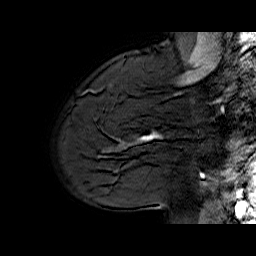
Breast MRI (dynamic contrast-enhanced), one sagittal slice. Slice 50 of 70 in the series (ordered by position). Dynamic contrast-enhanced series, time point 2 of 6 at this slice position (early post-contrast). 1.5 T. TE 6.5 ms, TR 33 ms. 4 mm slice thickness. 256 × 256 image matrix, field of view 200 × 200 mm. Female patient. From the clinical record (not read from this slice): setting: breast cancer imaged before/during neoadjuvant chemotherapy; receptor status: HER2-positive.
Outlined on this slice (semi-automatic segmentation, software-assisted and operator-edited):
- analysis volume of interest (the breast-tissue region the enhancement analysis was run in; not a lesion): bounding box <113,112,174,170> (left, top, right, bottom; pixels)
- tumour enhancement mask (voxels above the 100 % enhancement threshold inside the analysis volume of interest): <139,134,157,141>